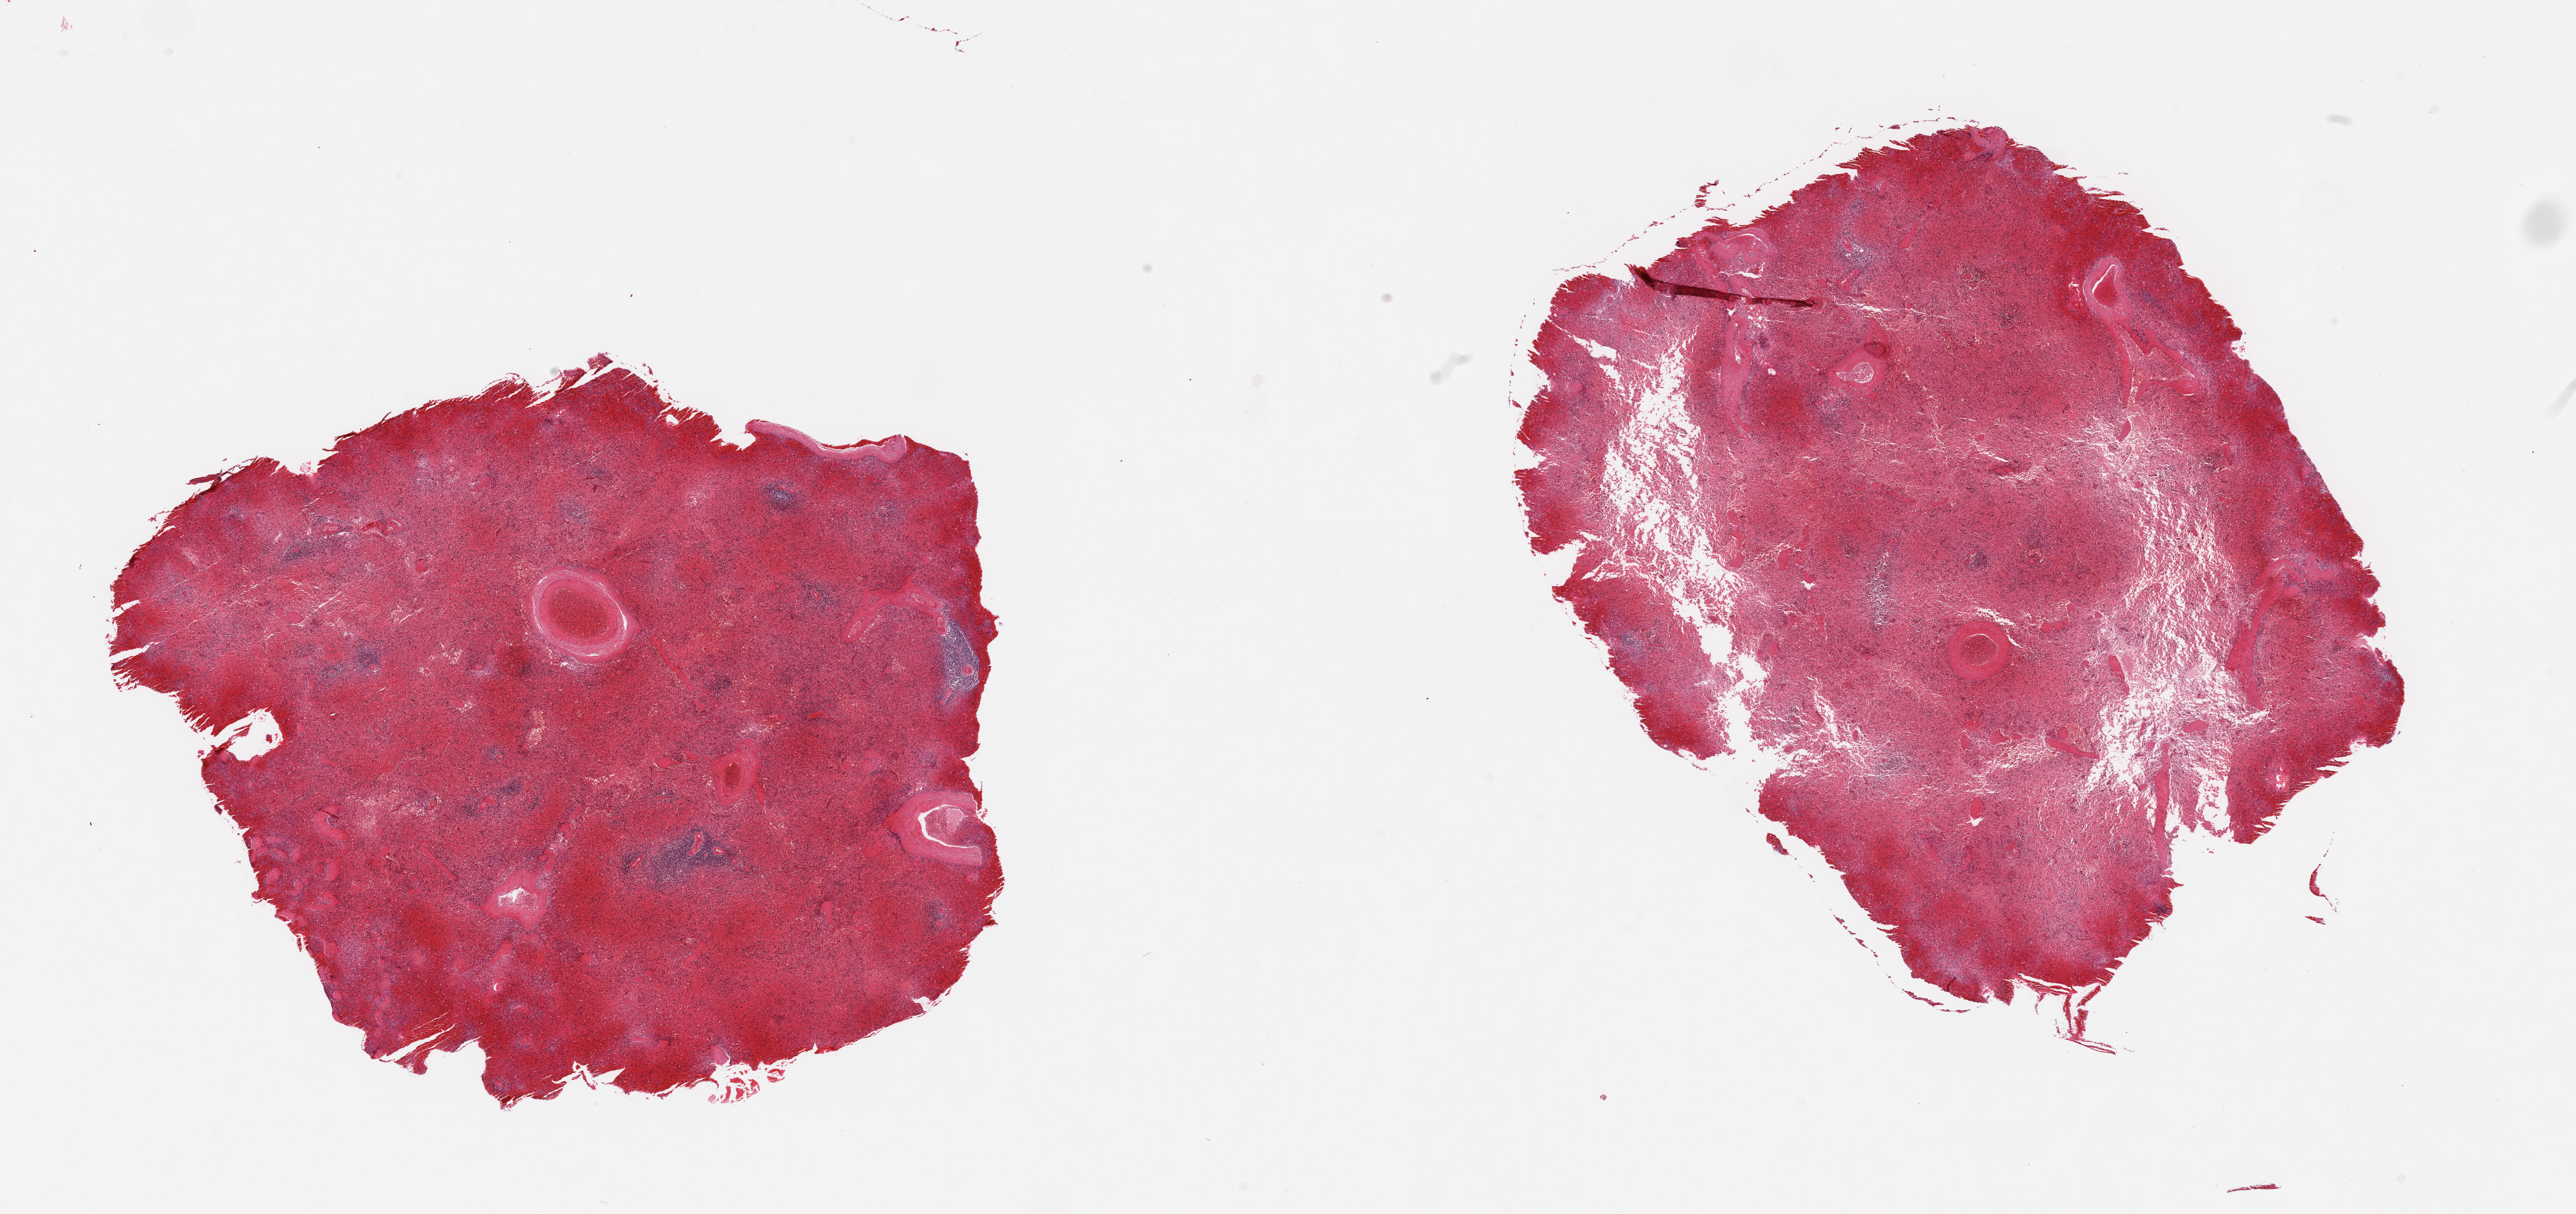
Digitized haematoxylin and eosin-stained section, brightfield — shown as a low-resolution overview of the whole scanned area (about 31.5 x 14.8 mm, from a 20x scan). PAXgene-fixed, paraffin-embedded tissue. Section of spleen (target tissue). Donor tissue sample. Male donor.
Reviewer comment on this tissue sample: 2 pieces, congested.